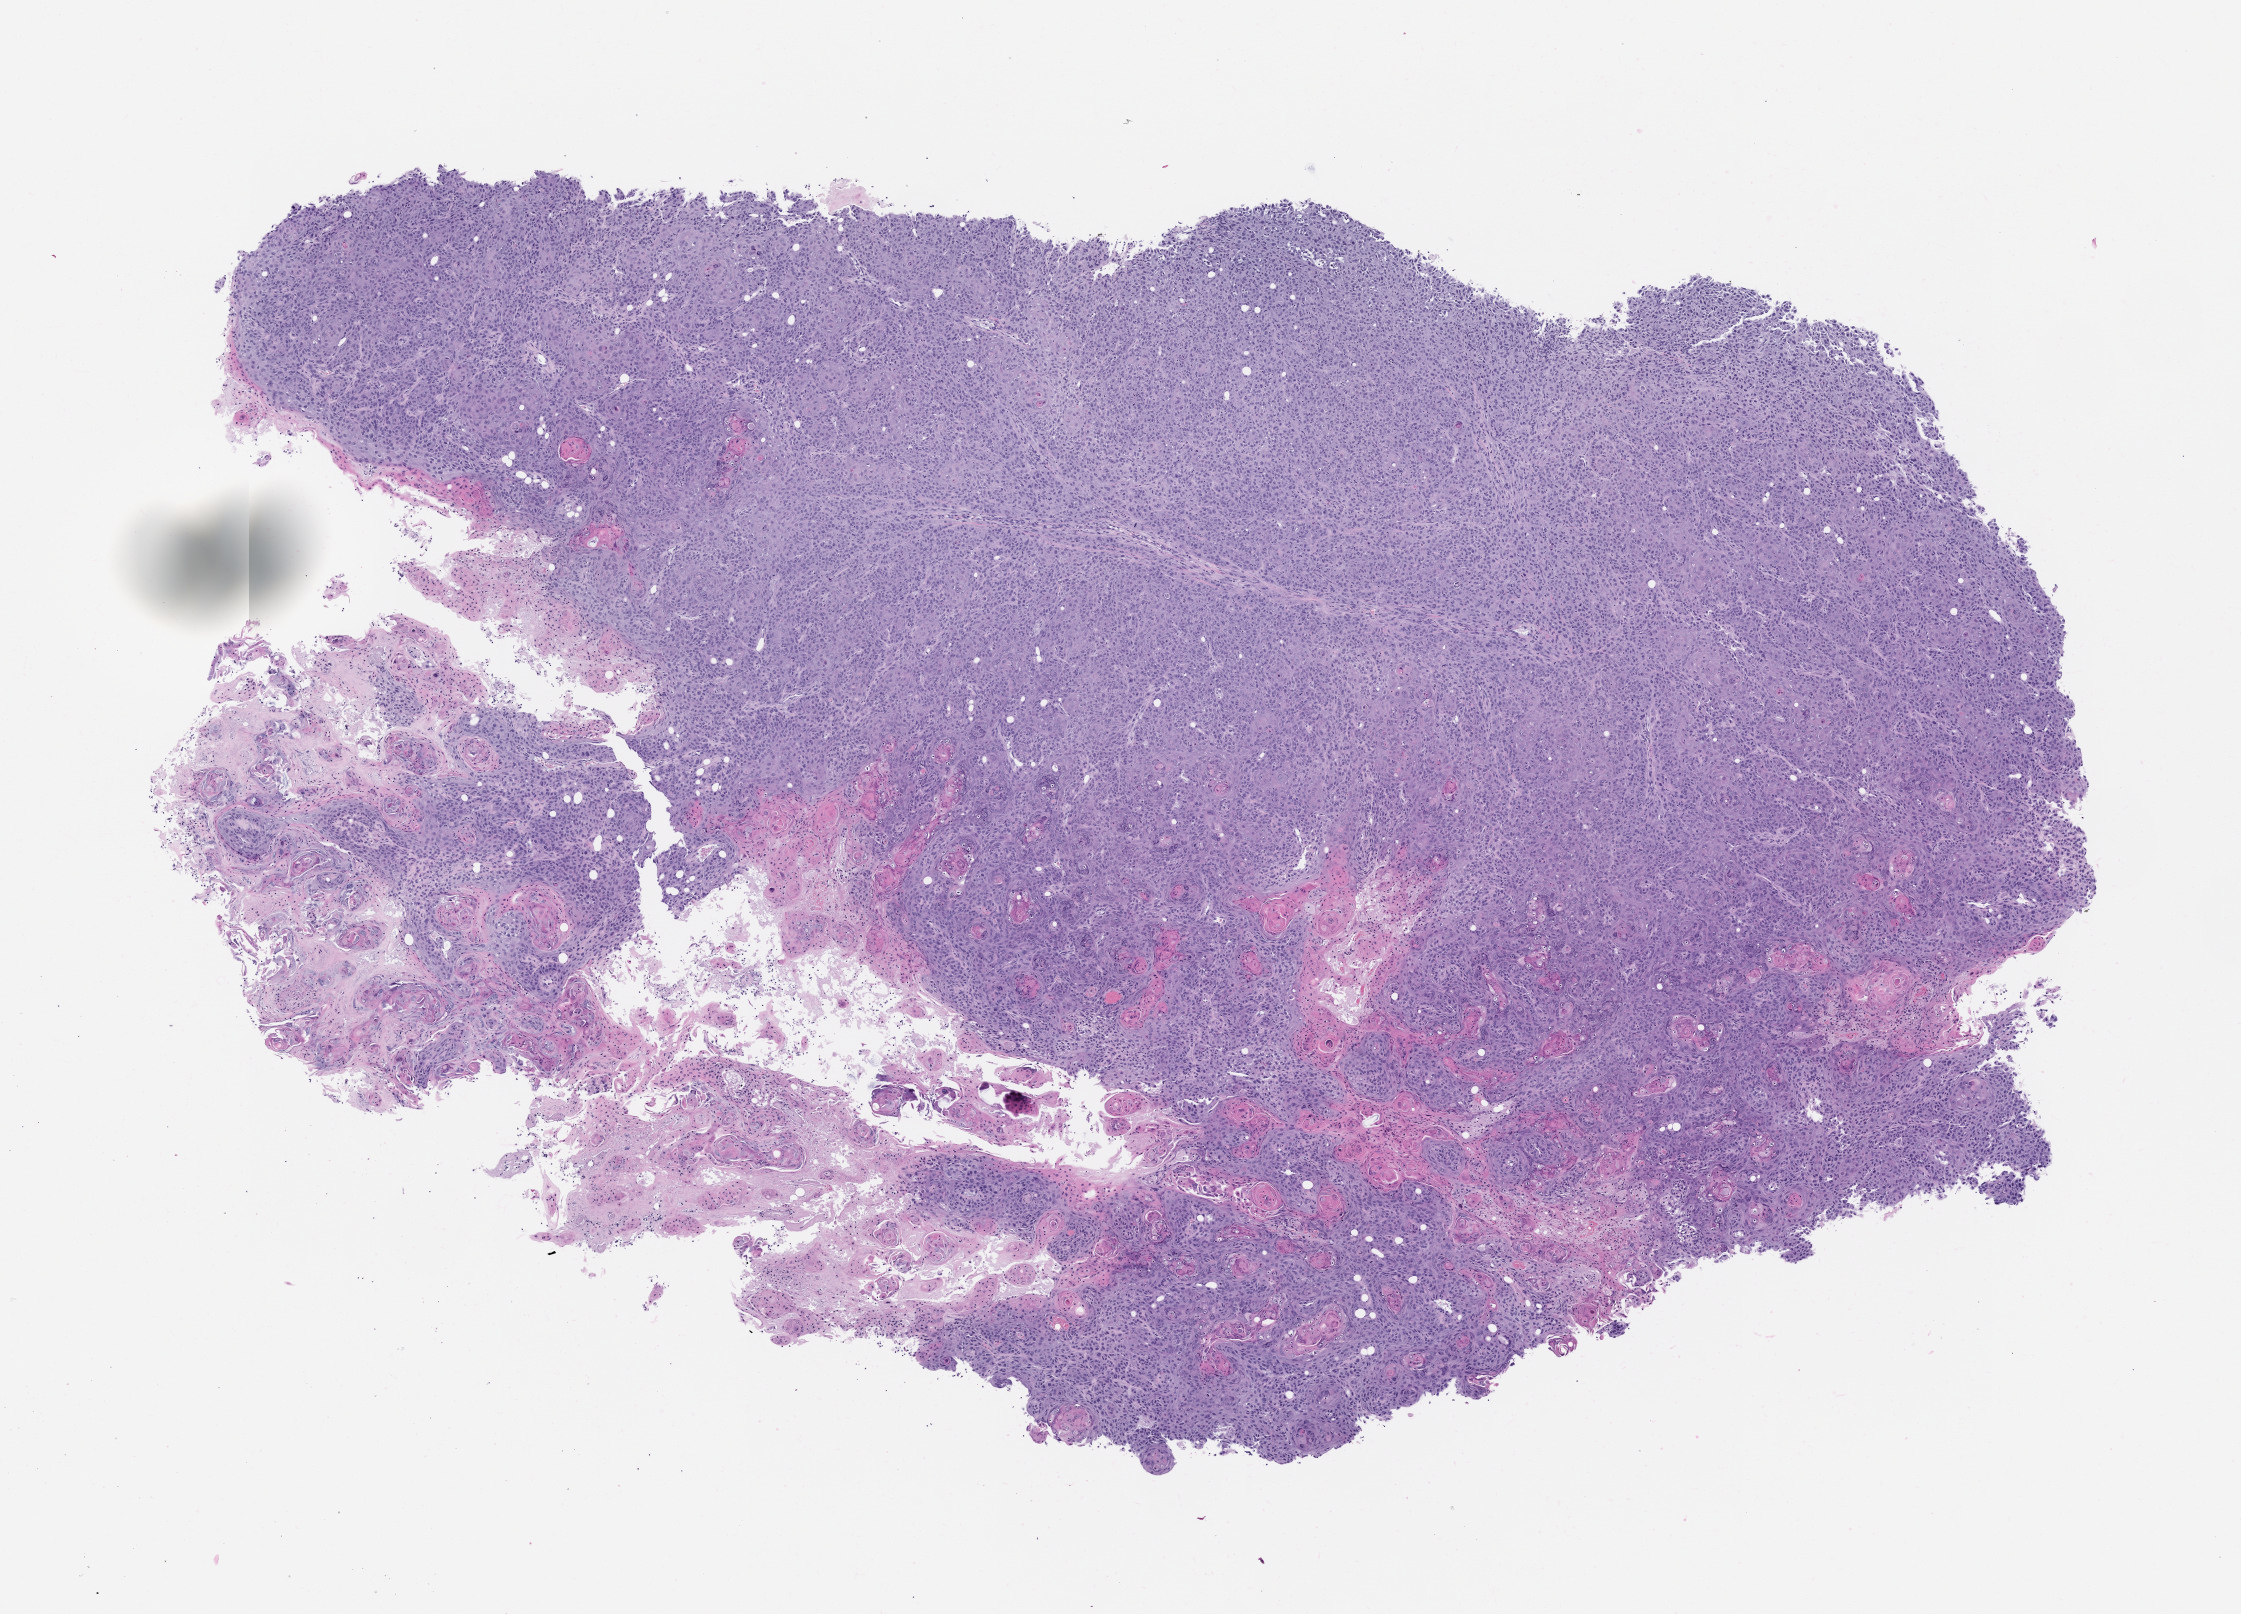
Haematoxylin and eosin whole-slide image of a patient-derived xenograft (PDX) tumor grown in a mouse, passage 2 — low-resolution overview of the scanned area, about 9.0 x 6.5 mm. Formalin-fixed, paraffin-embedded (FFPE) tissue. Tumor site category: oral soft tissue.
Originating patient diagnosis: Head and Neck Squamous Cell Carcinoma.